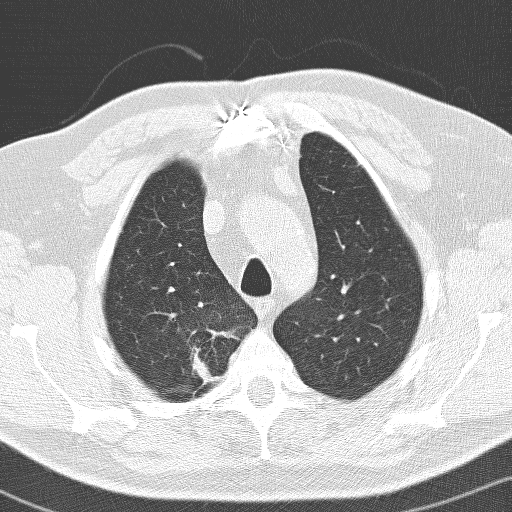
Chest CT (low-dose screening protocol), one axial image, first (baseline) screen, lung window (W 1500 / L -600 HU), lung (sharp) reconstruction kernel (D), slice 25 of 141 in the series. Male, age 66 years at enrolment. Former smoker at enrolment.
Expert reader's lesion annotation, box from (x=155, y=318) to (x=231, y=394) px. Screening reader's record for this exam (one nodule recorded; not confirmed to be the boxed lesion): non-calcified nodule or mass ≥4 mm, right upper lobe, 36 × 30 mm, spiculated (stellate) margins, soft tissue attenuation. Lung cancer was diagnosed 103 days after this screen: adenocarcinoma, NOS, right upper lobe, poorly differentiated (G3), stage IIB (AJCC 6th edition), 33 mm at pathology.